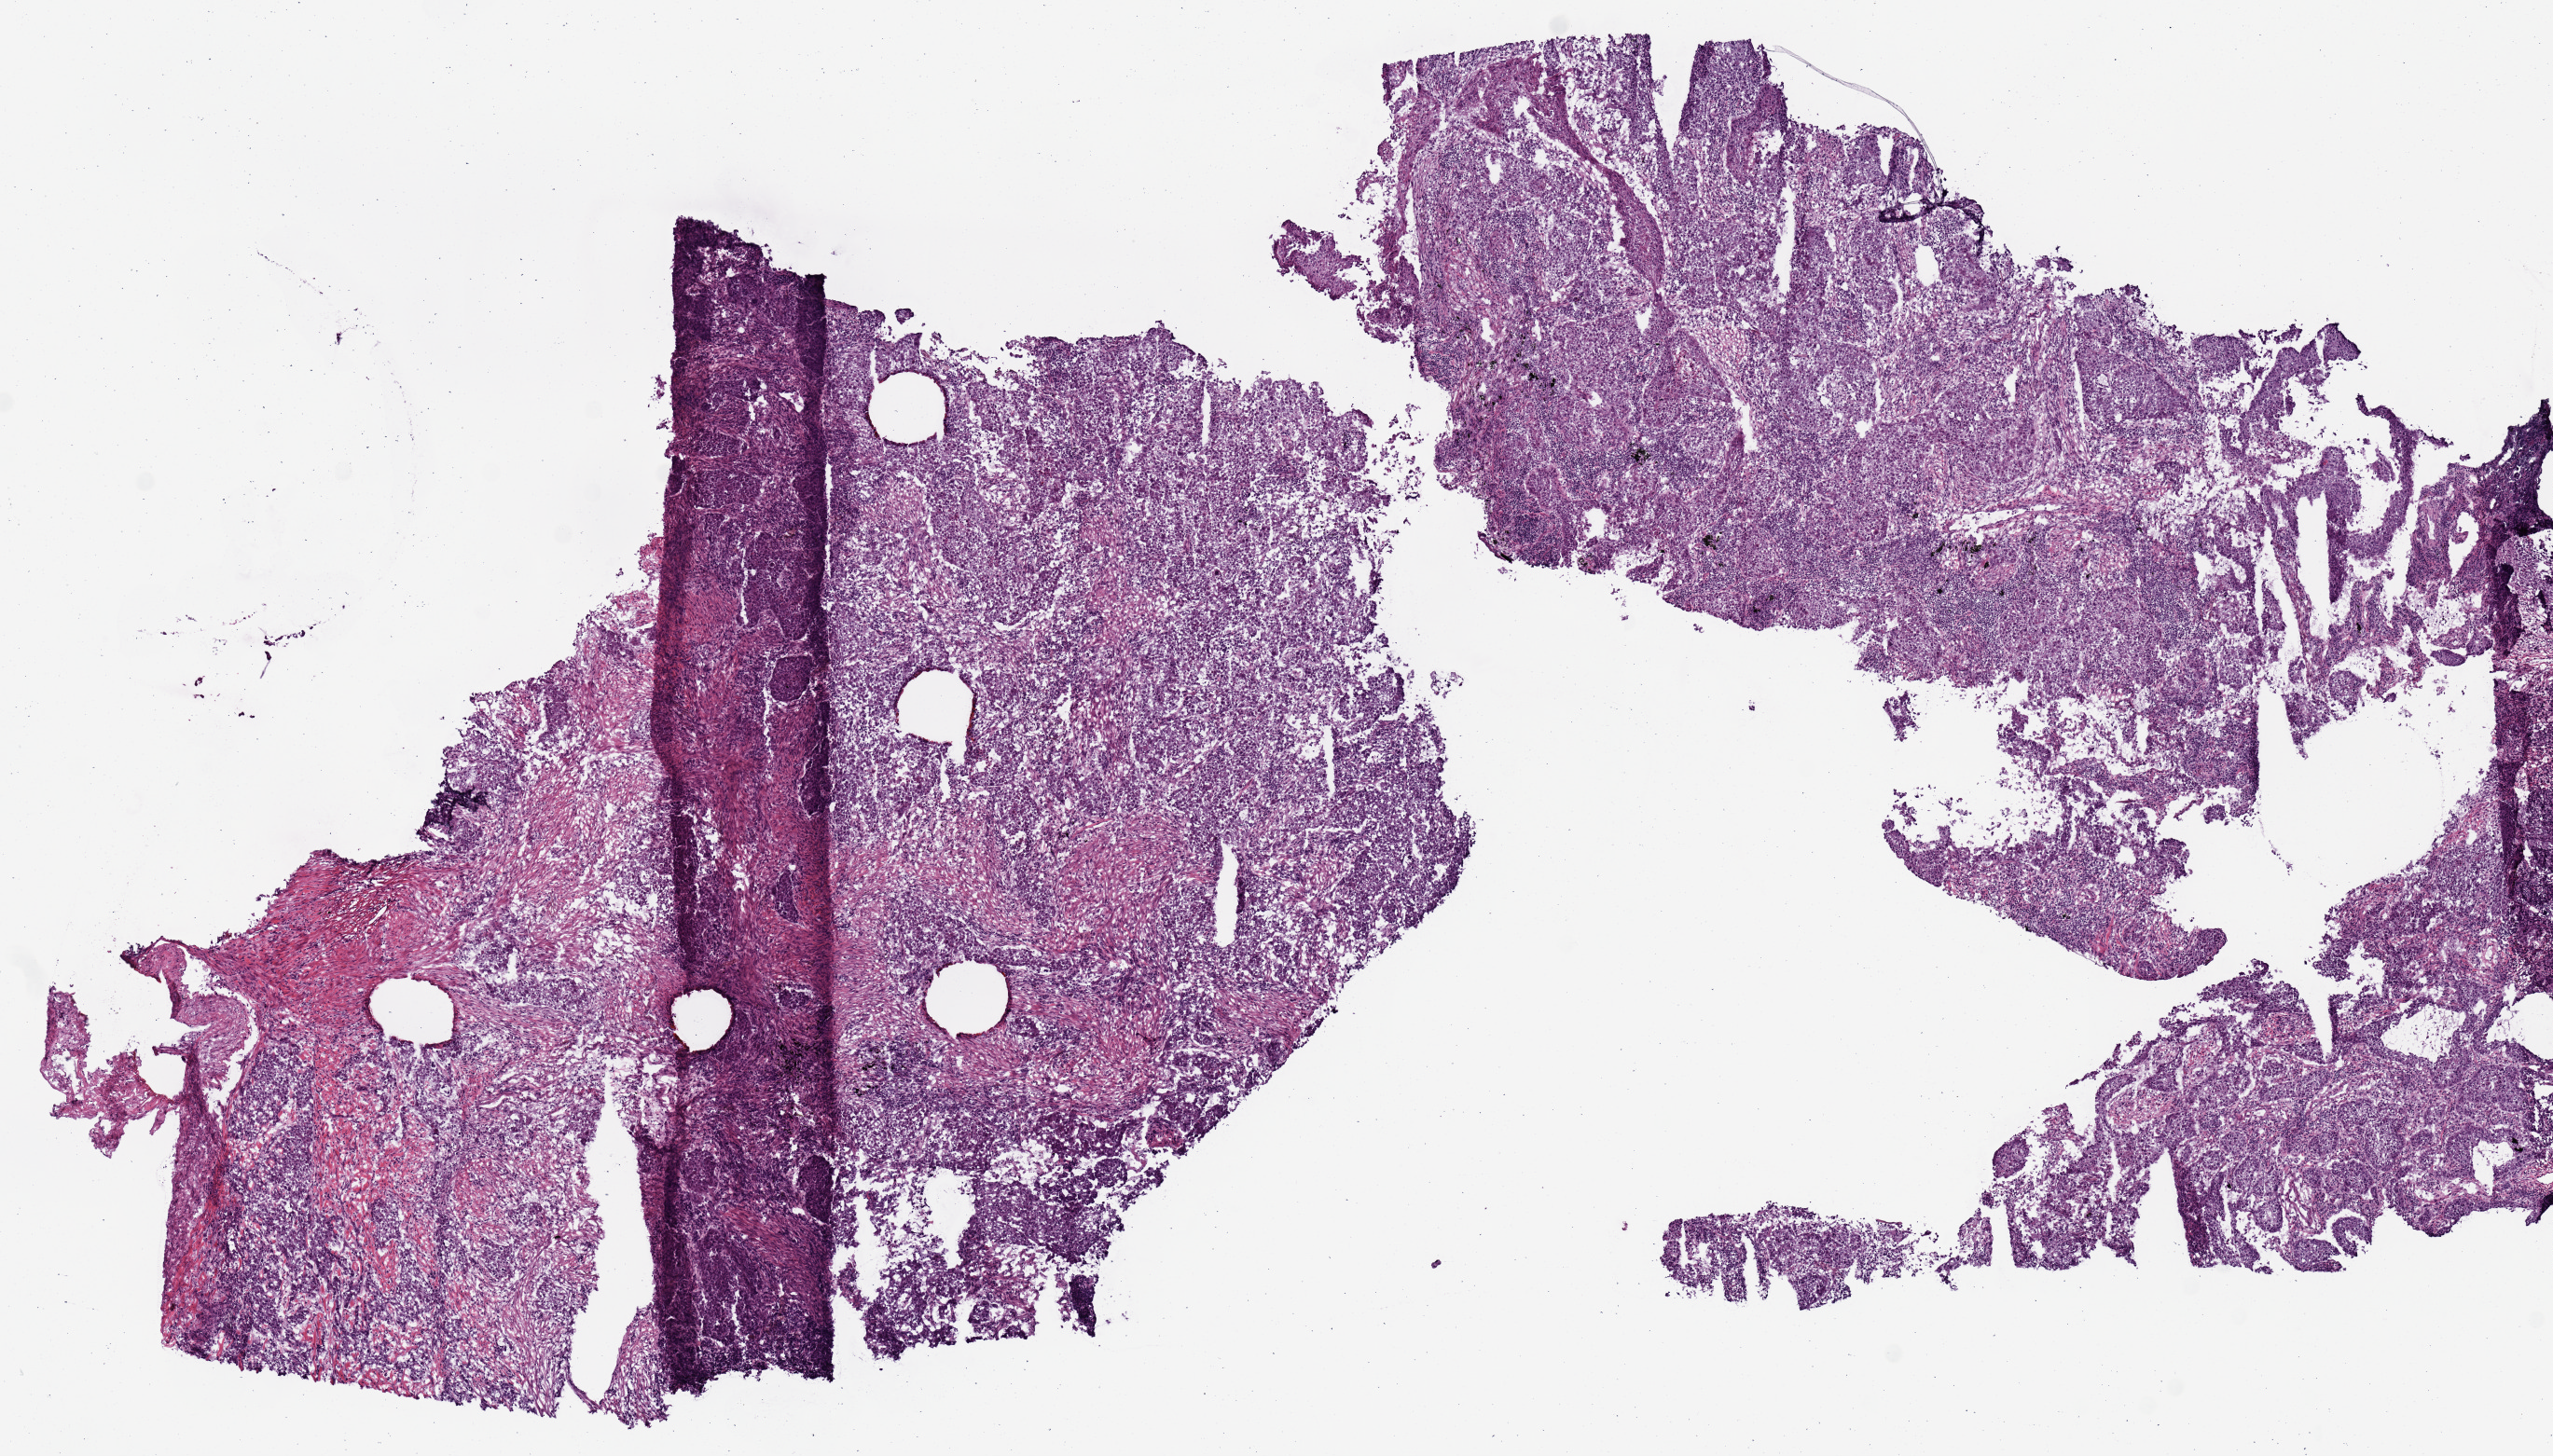
Digitized H&E-stained tissue section (whole slide), shown as a low-resolution overview of the whole scanned area (about 10.8 x 6.2 mm, from a 20x scan). Frozen section from the top of the tissue portion. Lung, primary tumour sample. Male patient; age at initial diagnosis 73 years. Composition of this section per pathologist review: tumour nuclei 65%, necrosis 0%.
* AJCC pathologic stage: IIA (7th edition)
* laterality: right
* pathologic diagnosis: Squamous cell carcinoma, NOS